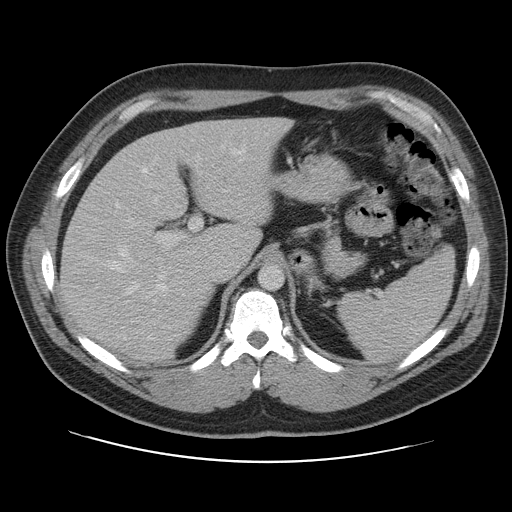
Contrast-enhanced abdominal CT, one axial slice. Position 76 of 109 along the scan axis. 120 kVp. Soft-tissue window (W 400 / L 40 HU). 5 mm slice thickness. 512 × 512 image matrix, field of view 402 × 402 mm. Male patient, age 35 years. Case-level facts recorded for this patient, not image findings: diagnosis: colorectal cancer liver metastases, imaged before liver resection; multiple liver metastases: yes.
Annotated regions visible in this slice (expert manual segmentation):
- hepatic veins: box from (x=103, y=148) to (x=245, y=294) px
- liver: (x=62, y=119)–(x=287, y=361)
- planned liver remnant (the part of the liver to remain after resection): (x=62, y=119)–(x=281, y=359)
- portal vein (with intrahepatic branches): (x=118, y=160)–(x=203, y=299)